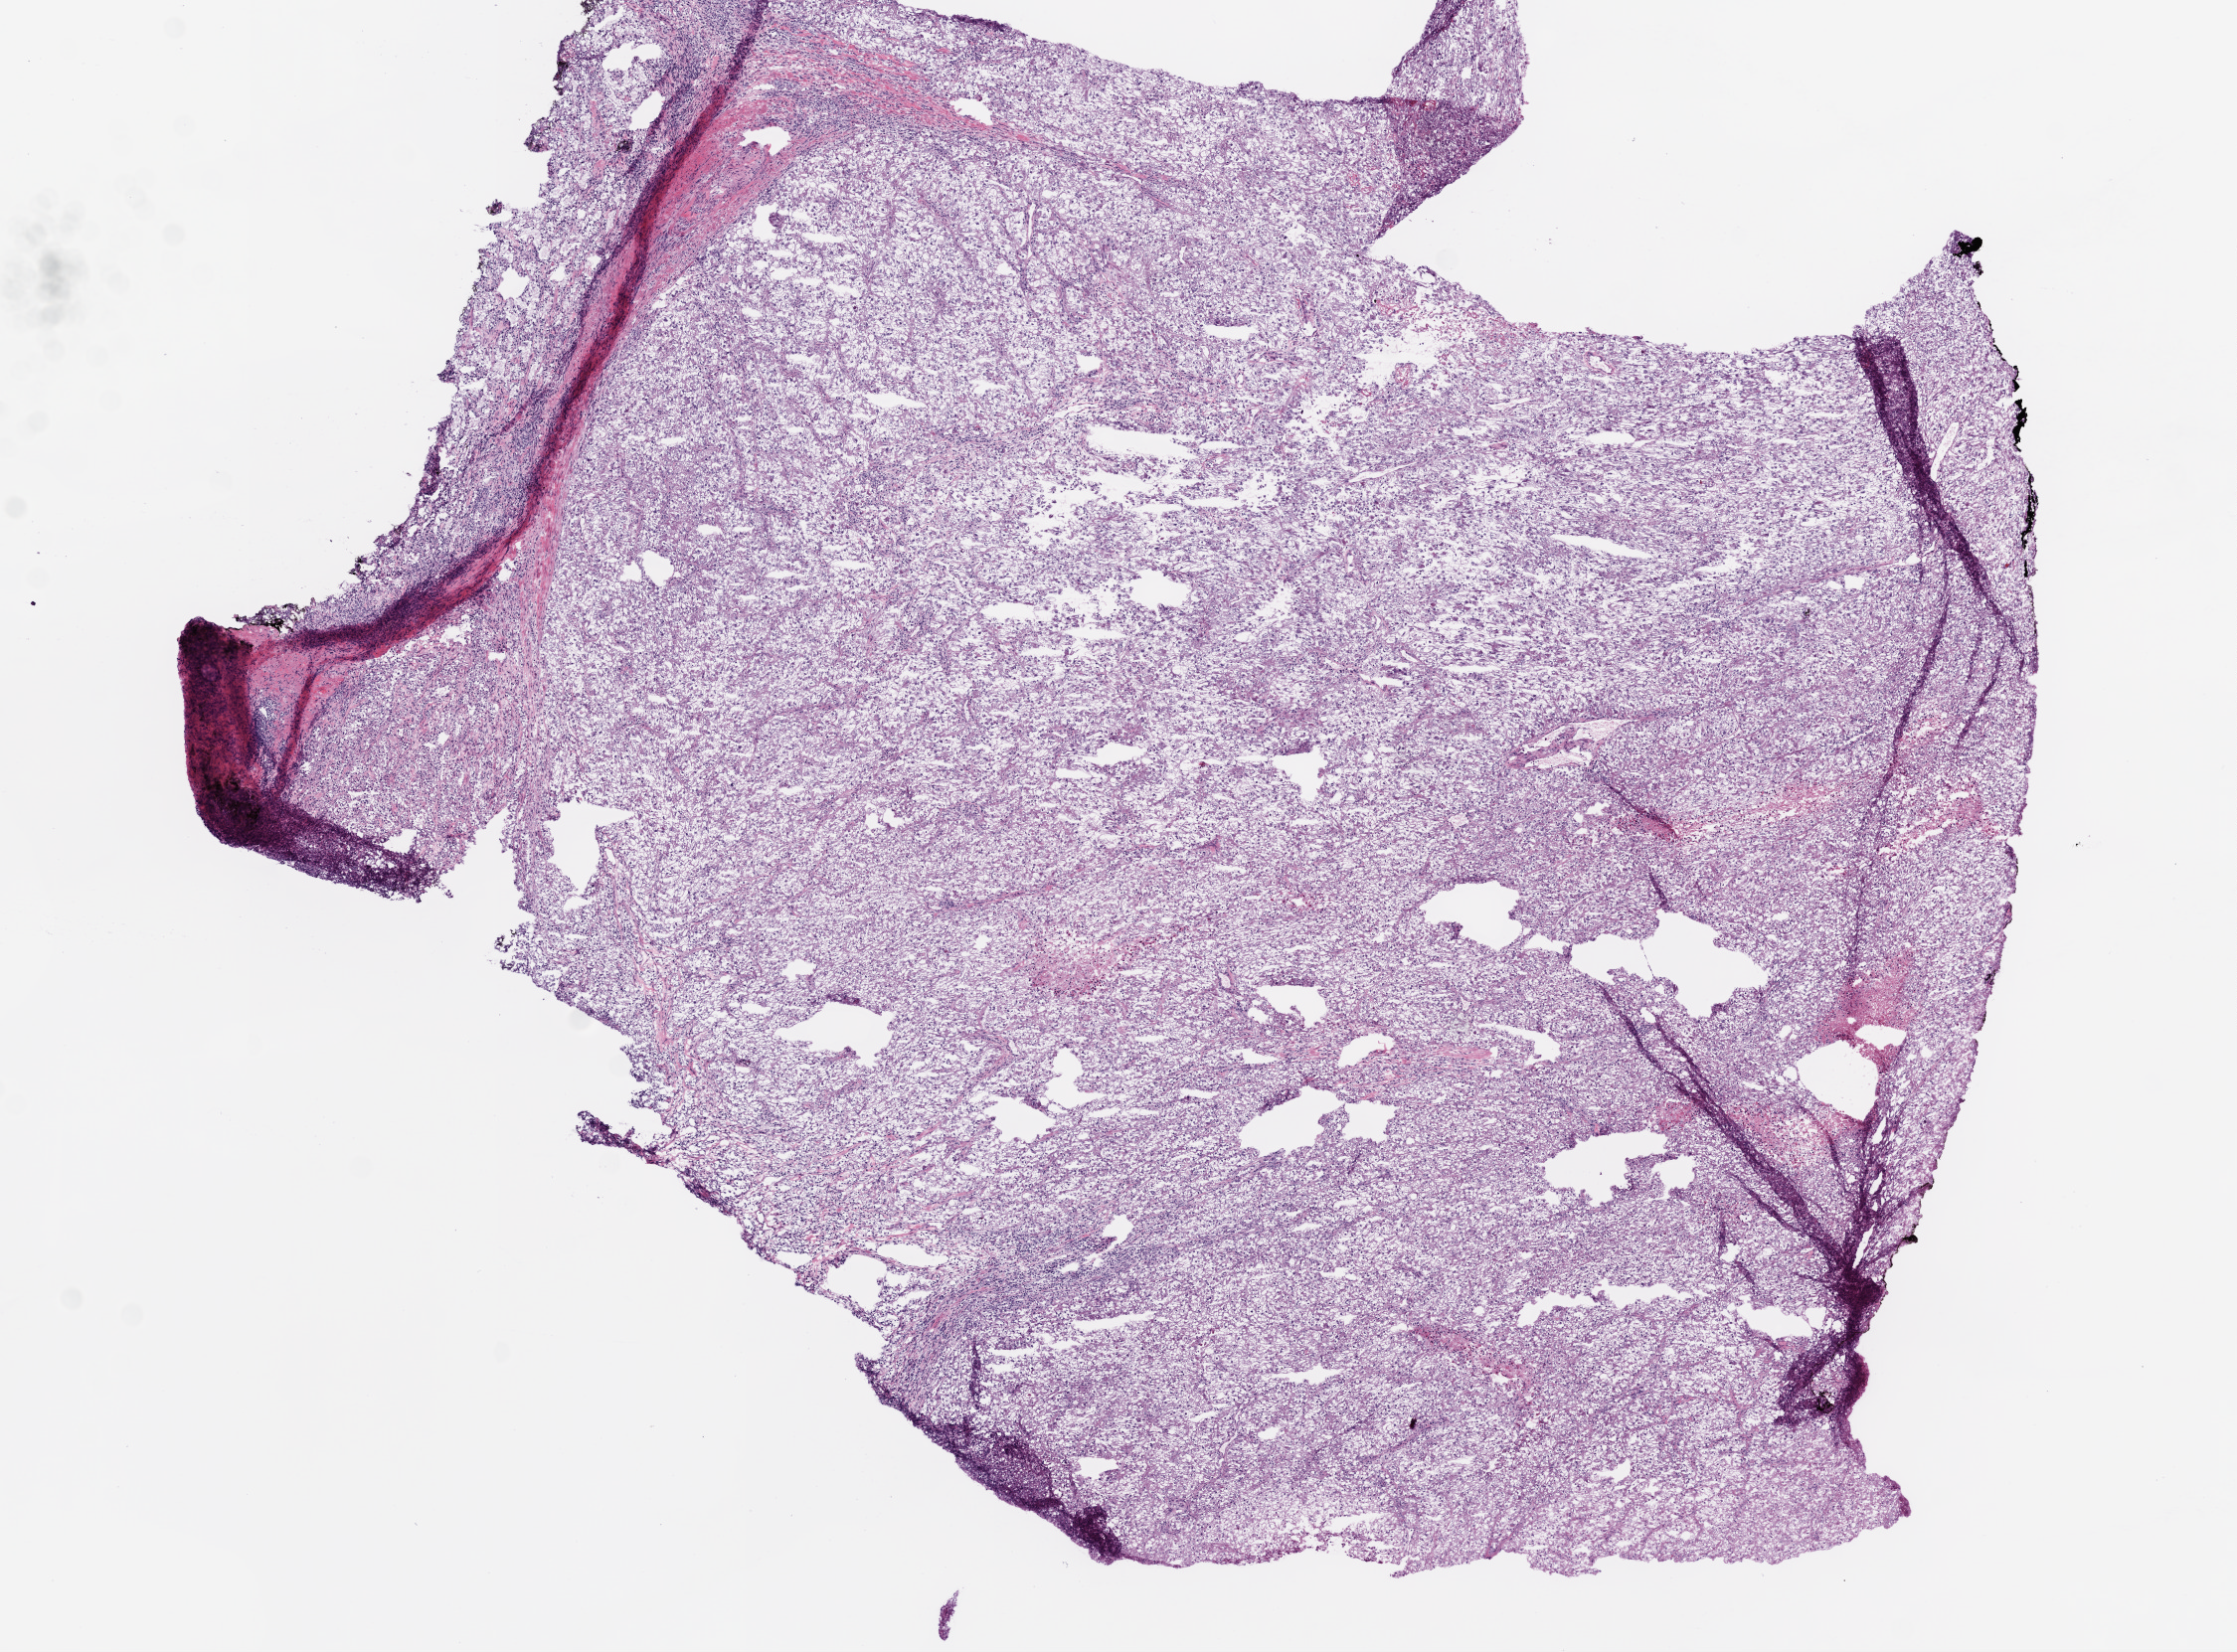
H&E whole-slide image — whole scanned area (about 9.0 x 6.7 mm, slide scanned at 20x) shown as a low-resolution overview; frozen section from the top of the tissue portion; sample: primary tumour, kidney. Male, age 70 years at initial diagnosis. Histologic grade: G2 (moderately differentiated). Slide review estimates, as recorded: tumour cells 95%, tumour nuclei 85%, normal cells 0%, stromal cells 5%, necrosis 0%.
• AJCC pathologic stage: I
• pathologic diagnosis: Clear cell adenocarcinoma, NOS